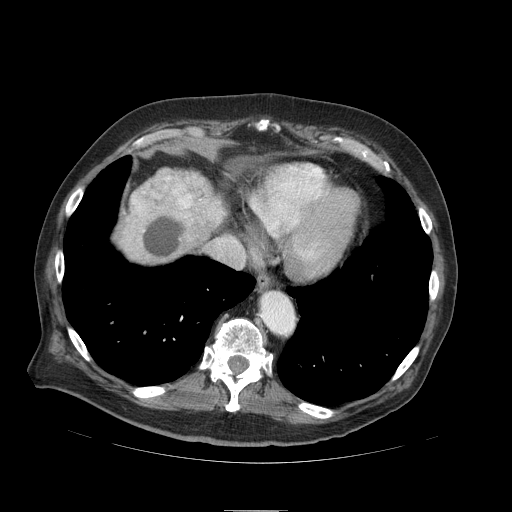
Contrast-enhanced abdominal CT (liver protocol), one axial slice. Slice 82 of 103 in the series (ordered by position). Reconstruction kernel STANDARD. 120 kVp. Soft-tissue window (W 400 / L 40 HU). 512 × 512 image matrix, field of view 440 × 440 mm. From the clinical record (not read from this slice): diagnosis: hepatocellular carcinoma (patient treated with transarterial chemoembolisation; whether this scan precedes or follows treatment is not stated here); TNM stage (as recorded): Stage-IIIA; Child-Pugh class: B; tumour differentiation: well differentiated; tumour nodularity: multinodular.
Annotated regions visible in this slice (semi-automatic segmentation, software-assisted and operator-edited):
- liver parenchyma outside the tumour (the mass and vessels are separate outlines, so this box may not span the whole liver): bounding box <116,168,226,264> (left, top, right, bottom; pixels)
- mass: <119,168,226,258>